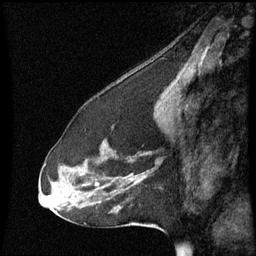
Breast MRI (dynamic contrast-enhanced), one sagittal slice; slice 27 of 60 in the series (ordered by position); dynamic contrast-enhanced series, image 2 of 3 at this slice position (ordered by acquisition); 1.5 T; TE 4.2 ms, TR 8.9 ms; 256 × 256 image matrix, field of view 200 × 200 mm. Patient: female, 53 years. Case-level facts recorded for this patient, not image findings: setting: breast cancer imaged before/during neoadjuvant chemotherapy; receptor status: HR-positive, HER2-negative.
Outlined on this slice (semi-automatic segmentation, software-assisted and operator-edited):
- analysis volume of interest (the breast-tissue region the enhancement analysis was run in; not a lesion): bounding box [x1, y1, x2, y2] px = [44, 120, 167, 223]
- tumour enhancement mask (voxels above the 70 % enhancement threshold inside the analysis volume of interest): [134, 180, 139, 185]